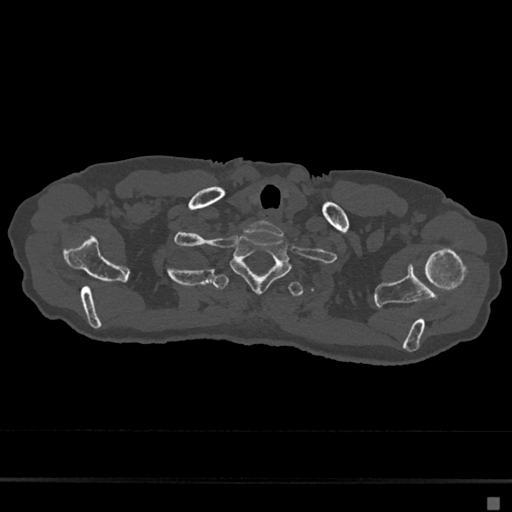
CT including the spine, one axial slice; position 604 of 797 along the scan axis; reconstruction kernel Br40s/3; 120 kVp; bone window (W 1800 / L 400 HU); 0.5 mm slice thickness; 512 × 512 image matrix, field of view 360 × 360 mm. Patient: female, 68 years. Case-level facts recorded for this patient, not image findings: primary cancer: renal.
Structures marked on this image (semi-automatic segmentation, software-assisted and operator-edited):
- T1 vertebra: bounding box [x1, y1, x2, y2] px = [230, 235, 291, 293]
- T2 vertebra: [212, 274, 304, 297]